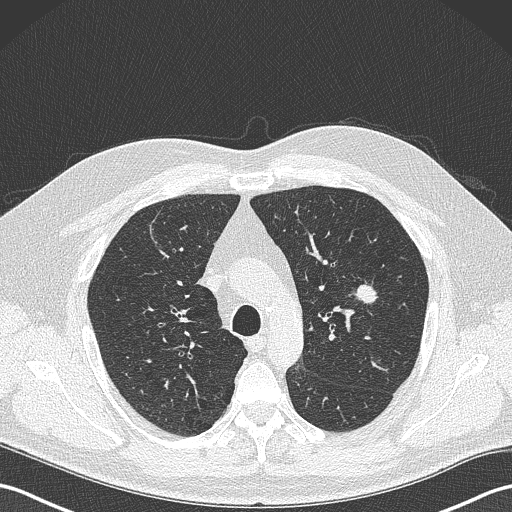
Low-dose screening chest CT, one axial slice; position 245 of 343 along the scan axis; 120 kVp; lung window (W 1500 / L -600 HU); 512 × 512 image matrix, field of view 350 × 350 mm.
Structures marked on this image (manually delineated by an expert):
- lesion 1 (tumor, upper lobe of left lung): bounding box <355,281,378,304> (left, top, right, bottom; pixels)